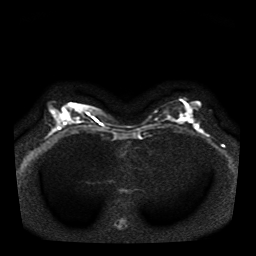
Breast MRI, one axial slice. Slice 20 of 41 in the series (ordered by position). Diffusion-weighted series; image 2 of 4 stored at this slice position (different b-values; order by instance number). 1.5 T. 5 mm slice thickness. 256 × 256 image matrix, field of view 330 × 330 mm. Female patient.
Annotated regions visible in this slice (expert manual segmentation):
- tumour on diffusion-weighted imaging: bounding box <187,116,192,122> (left, top, right, bottom; pixels)